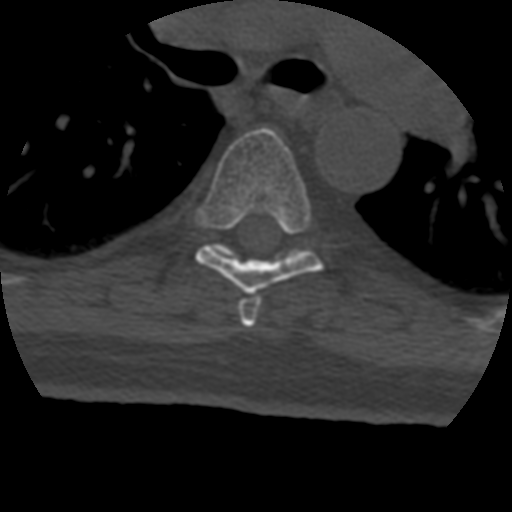
CT including the spine, one axial slice; slice 299 of 399 in the series (ordered by position); 120 kVp; bone window (W 1800 / L 400 HU); 512 × 512 image matrix, field of view 160 × 160 mm. Patient age 69 years. Case-level facts recorded for this patient, not image findings: primary cancer: prostate.
Structures marked on this image (semi-automatic segmentation, software-assisted and operator-edited):
- T5 vertebra: bounding box [x1, y1, x2, y2] px = [238, 289, 262, 327]
- T6 vertebra: [195, 128, 323, 294]
- T7 vertebra: [210, 243, 306, 259]